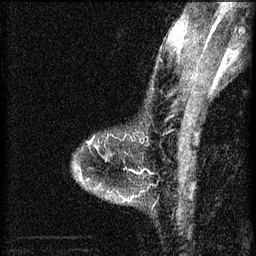
Breast MRI (dynamic contrast-enhanced), one sagittal slice. Position 49 of 60 along the scan axis. 3 images stored at this slice position (order not interpretable as contrast timing). 1.5 T. TE 4.2 ms, TR 8.2 ms. 2 mm slice thickness. 256 × 256 image matrix, field of view 180 × 180 mm. Patient: female, 46 years.
Annotated regions visible in this slice (semi-automatically segmented with operator editing):
- analysis volume of interest (the breast-tissue region the enhancement analysis was run in; not a lesion): bounding box (x1, y1, x2, y2) in pixels: (73, 136, 148, 205)
- tumour enhancement mask (voxels above the 70 % enhancement threshold inside the analysis volume of interest): (88, 142, 90, 145)